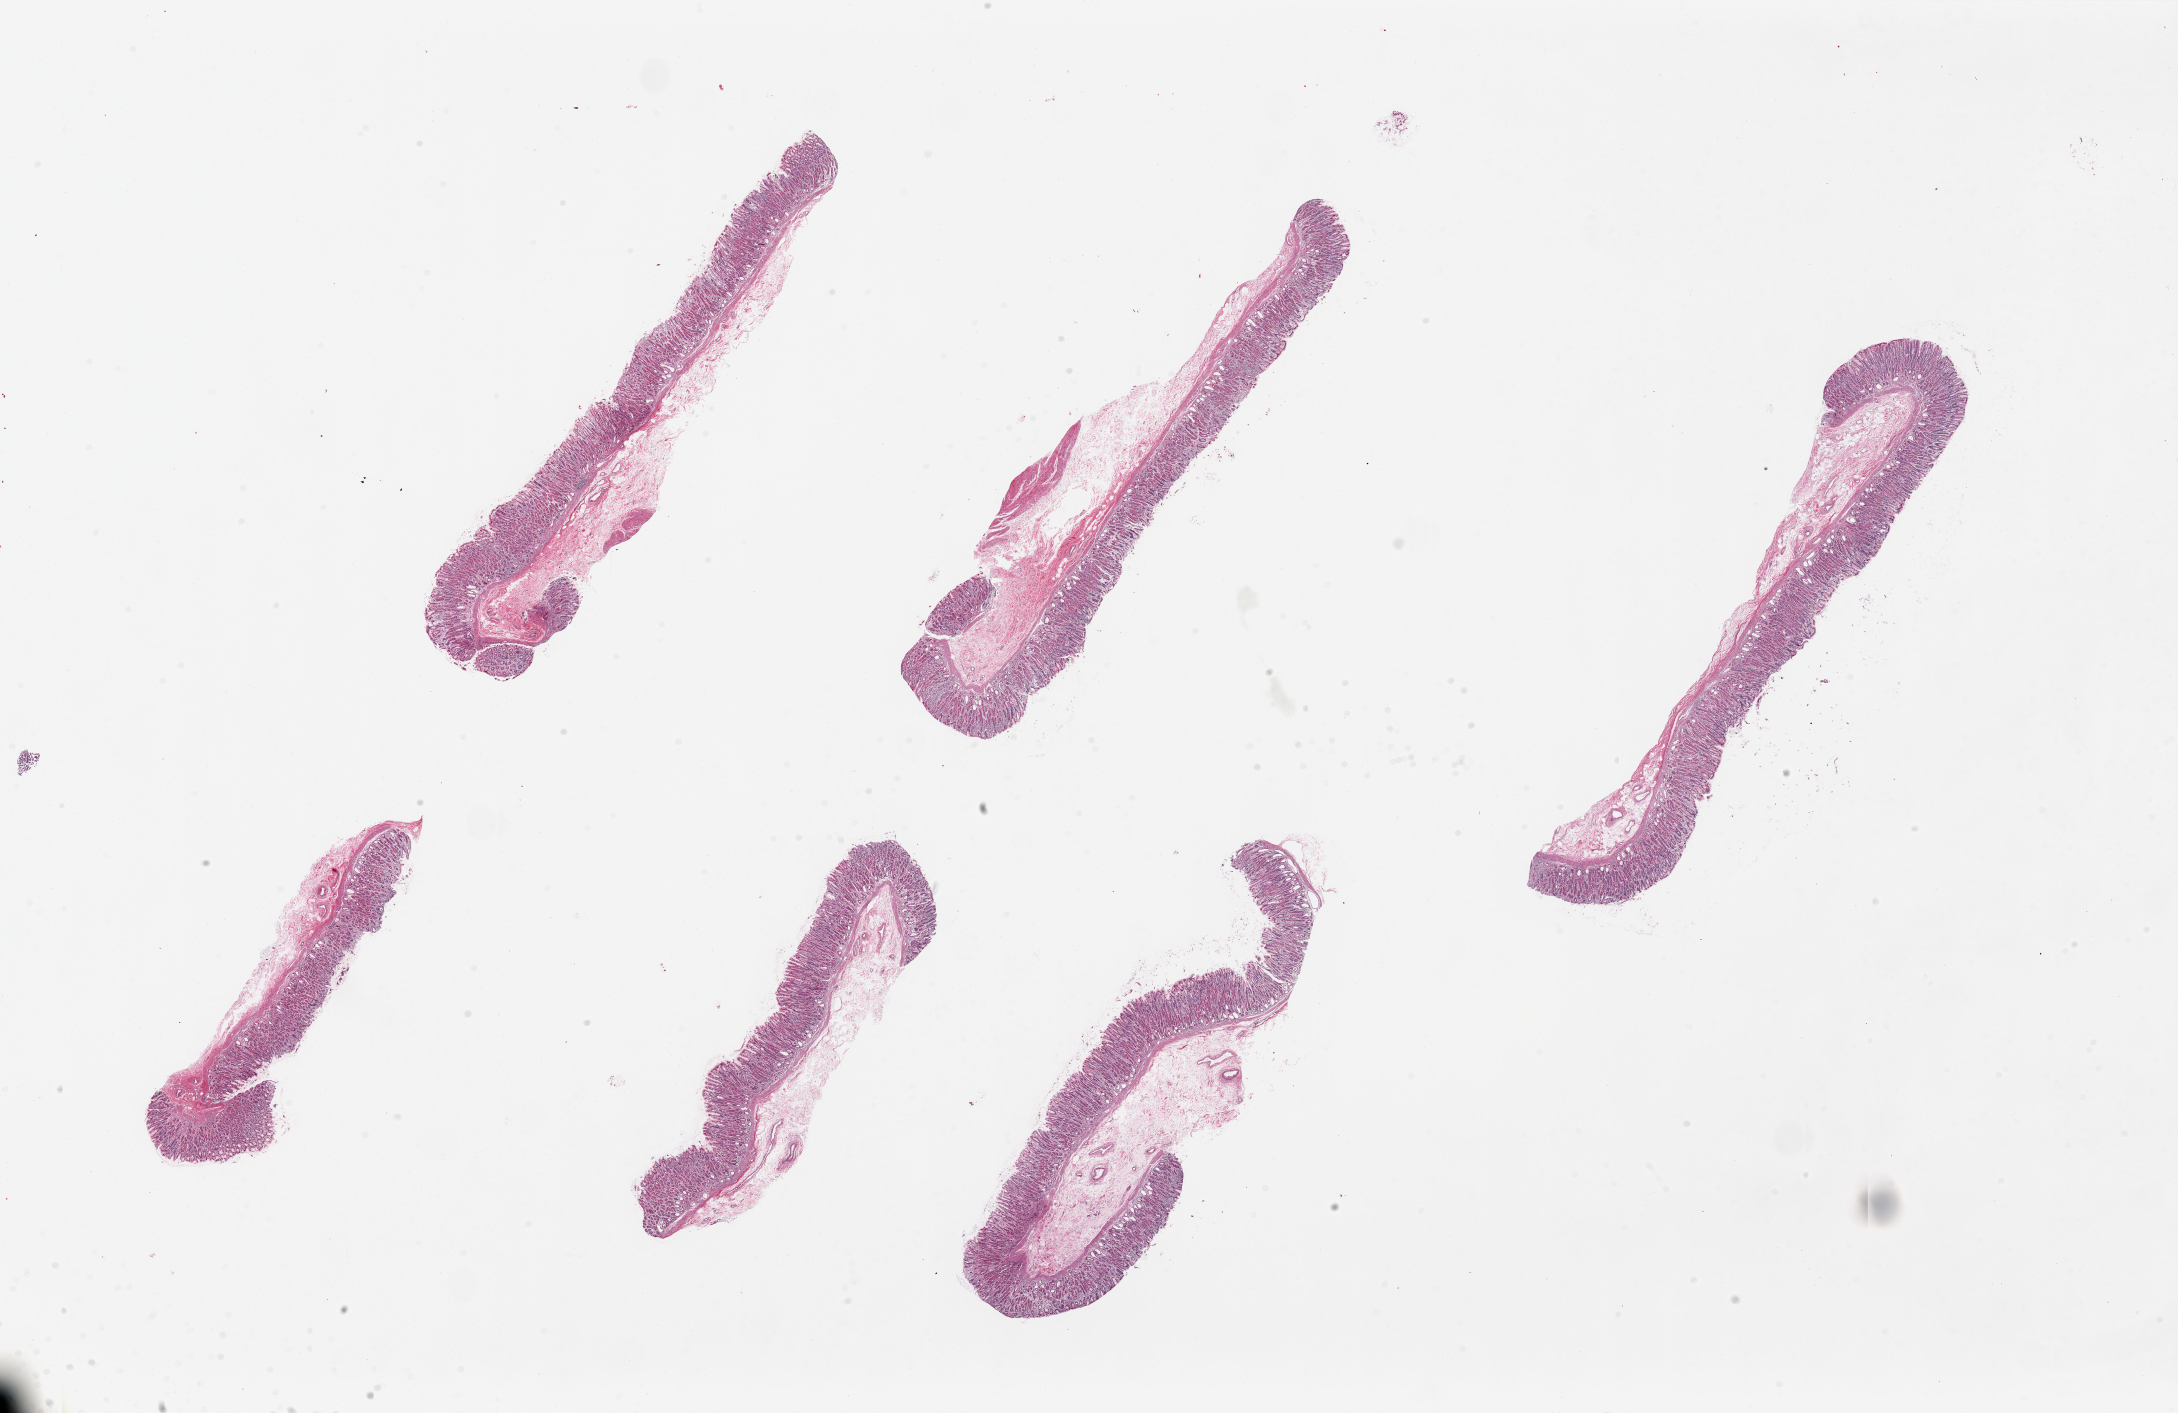
Whole-slide image, haematoxylin and eosin stain, whole scanned area (about 34.5 x 22.4 mm, slide scanned at 20x) shown as a low-resolution overview; PAXgene-fixed paraffin-embedded (PFPE) section; sampled site (target tissue): stomach; donor tissue sample. Donor: female.
Review note (as recorded): 6 pieces, up to 10x2mm; ~ up to ~30-70% mucosa in thickness, variably preserved.